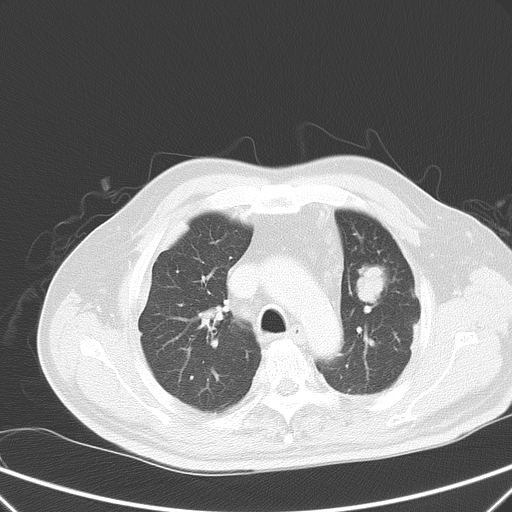
Chest CT, one axial slice. Position 43 of 59 along the scan axis. Intravenous contrast given. Lung window (W 1500 / L -600 HU). 512 × 512 image matrix, field of view 357 × 357 mm. Male patient, age 66 years. Case-level facts recorded for this patient, not image findings: clinical TNM (as recorded): T1c N3 M1a.
Annotated regions visible in this slice (rectangle marked by the reading radiologist):
- lung tumour (recorded histology: squamous cell carcinoma): bounding box (x1, y1, x2, y2) in pixels: (350, 261, 391, 307)